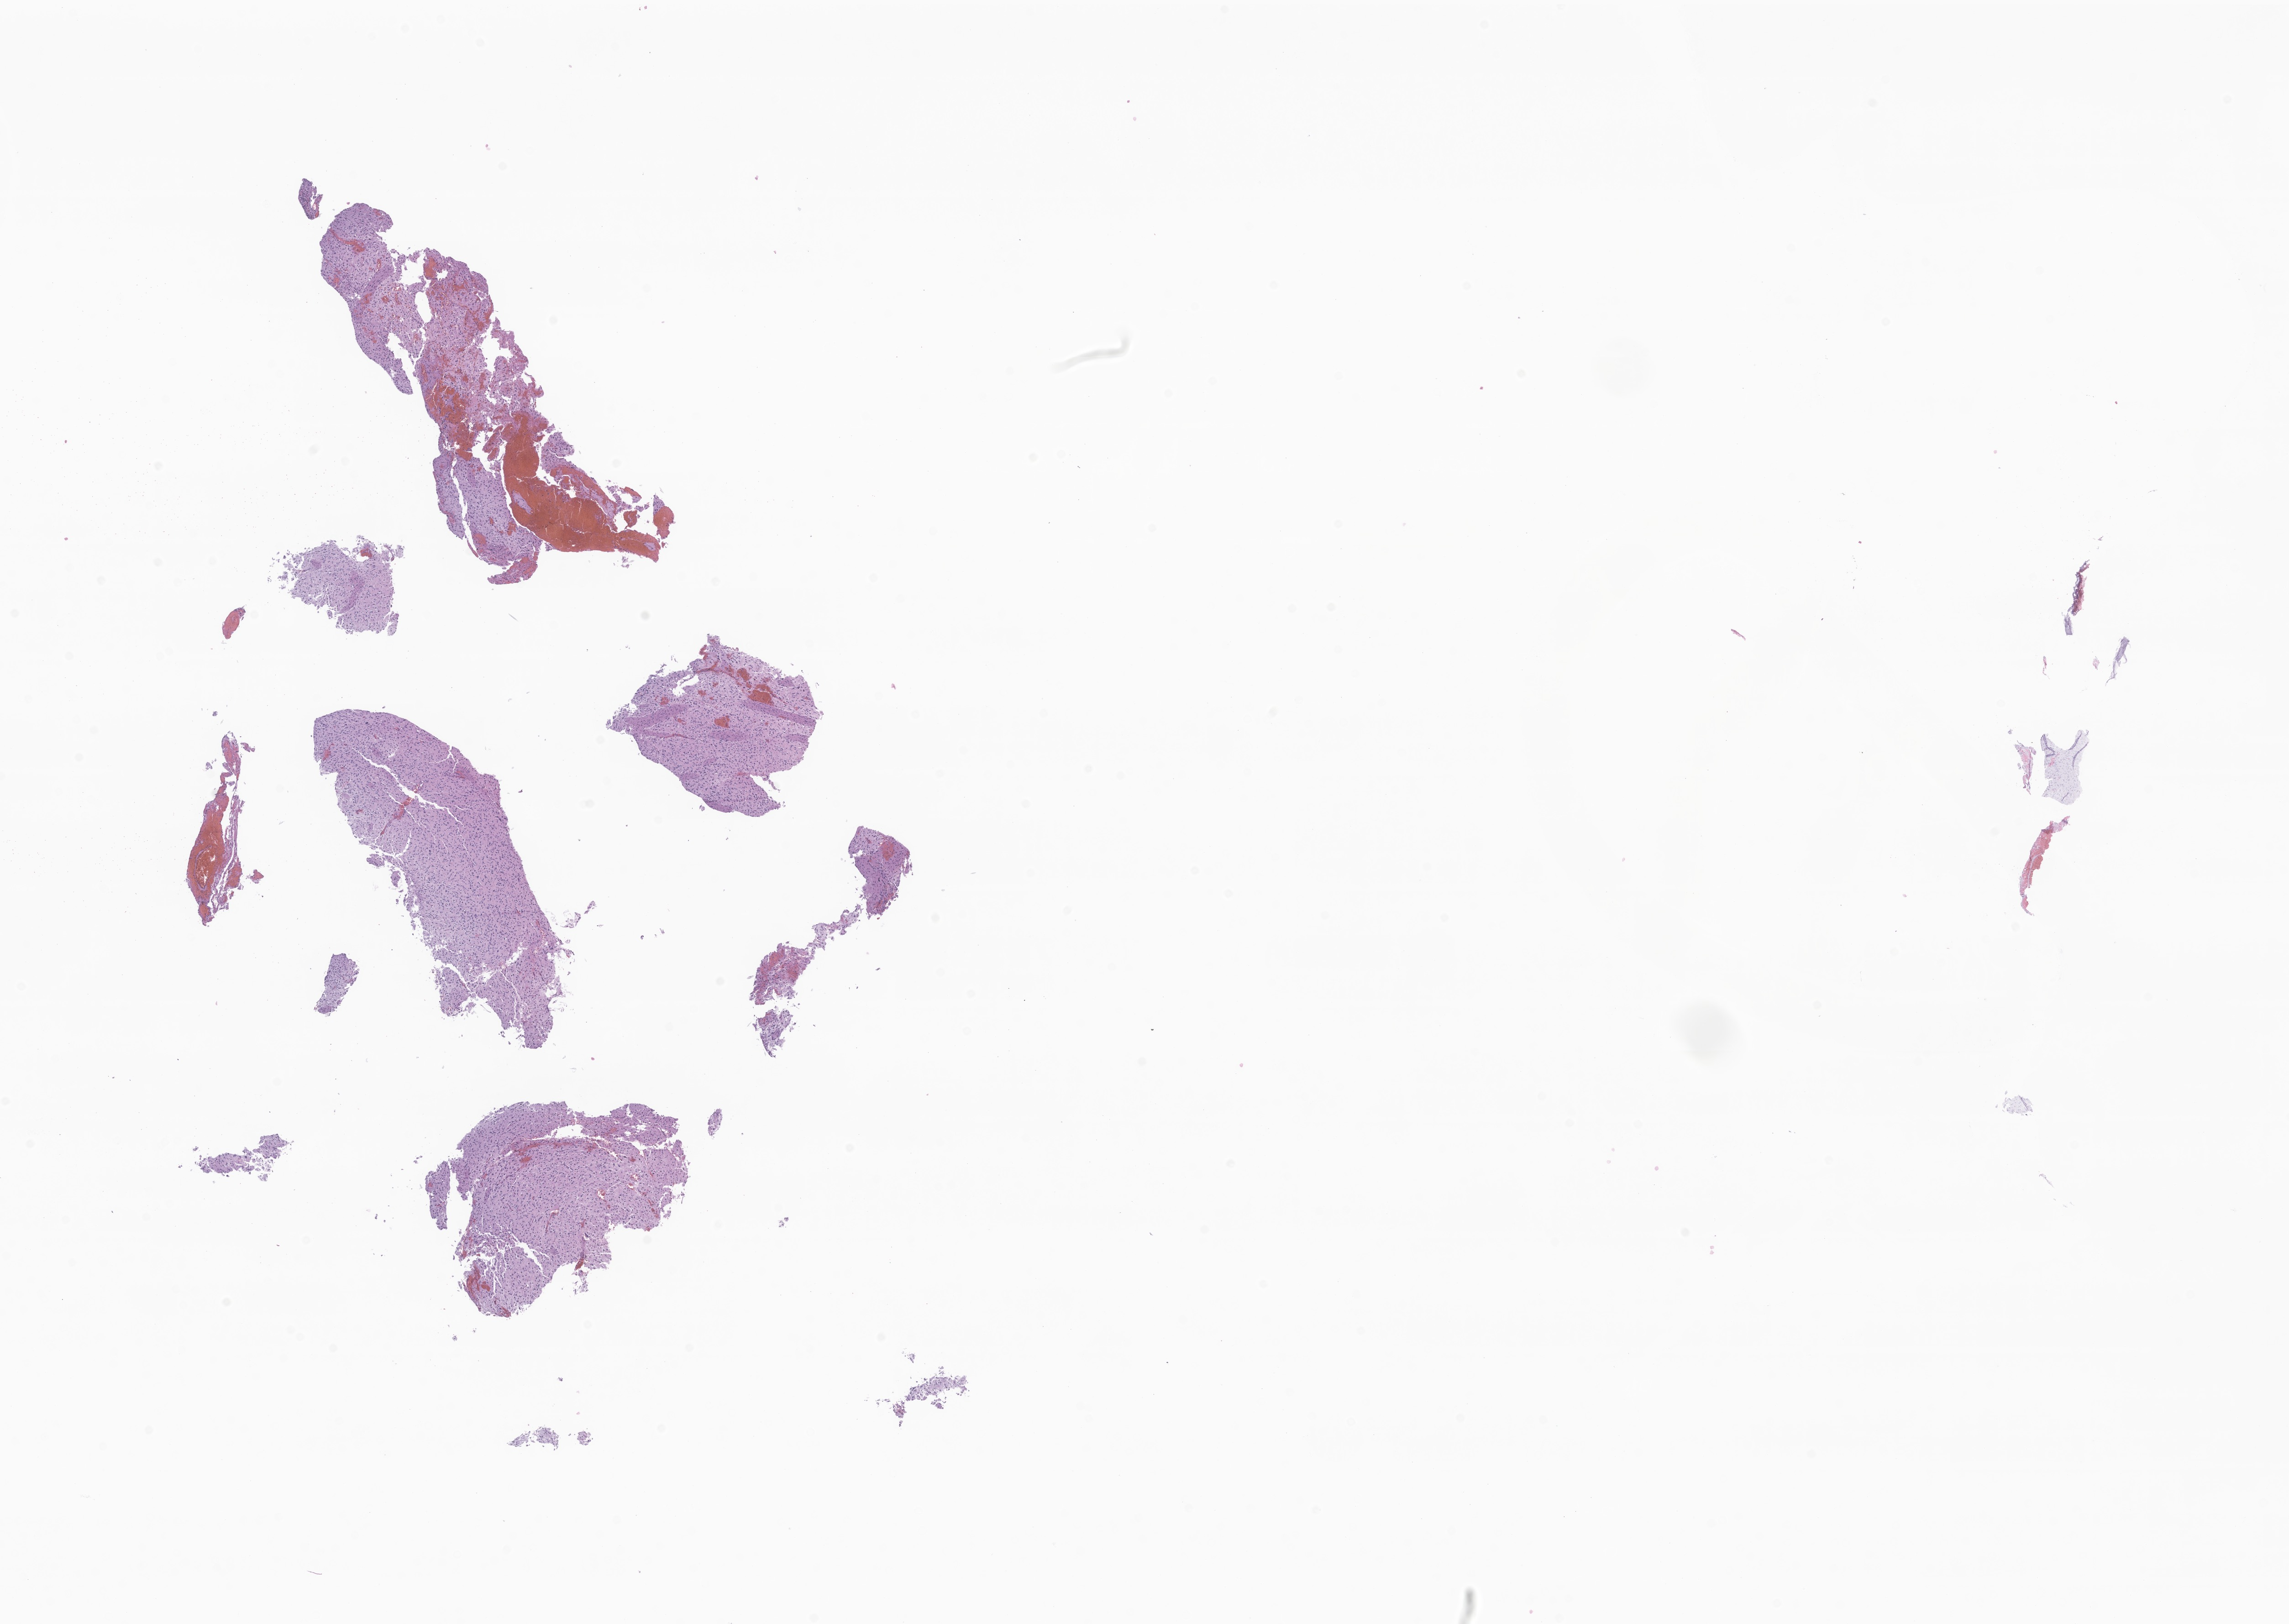
Whole-slide image, hematoxylin and eosin (H&E) stain of tumor tissue from the brain, shown as a low-resolution overview of the whole scanned area (about 21.1 x 15.0 mm). Formalin-fixed paraffin-embedded section. Patient: male, age 51 months (4 years 3 months).
Diagnosis: Glioma, malignant.